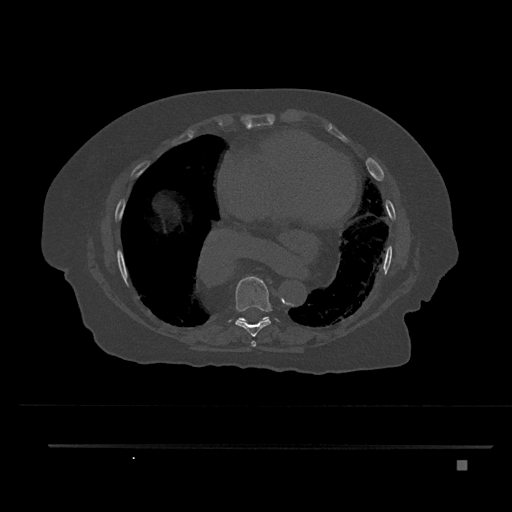
CT including the spine, one axial slice; position 434 of 797 along the scan axis; 120 kVp; bone window (W 1800 / L 400 HU); 0.5 mm slice thickness; 512 × 512 image matrix, field of view 437 × 437 mm. Patient: female, 76 years. Case-level facts recorded for this patient, not image findings: primary cancer: lung.
Structures marked on this image (semi-automatic segmentation, software-assisted and operator-edited):
- T7 vertebra: bounding box (x1, y1, x2, y2) in pixels: (251, 341, 256, 347)
- T8 vertebra: (235, 276, 272, 337)
- T9 vertebra: (238, 317, 268, 322)